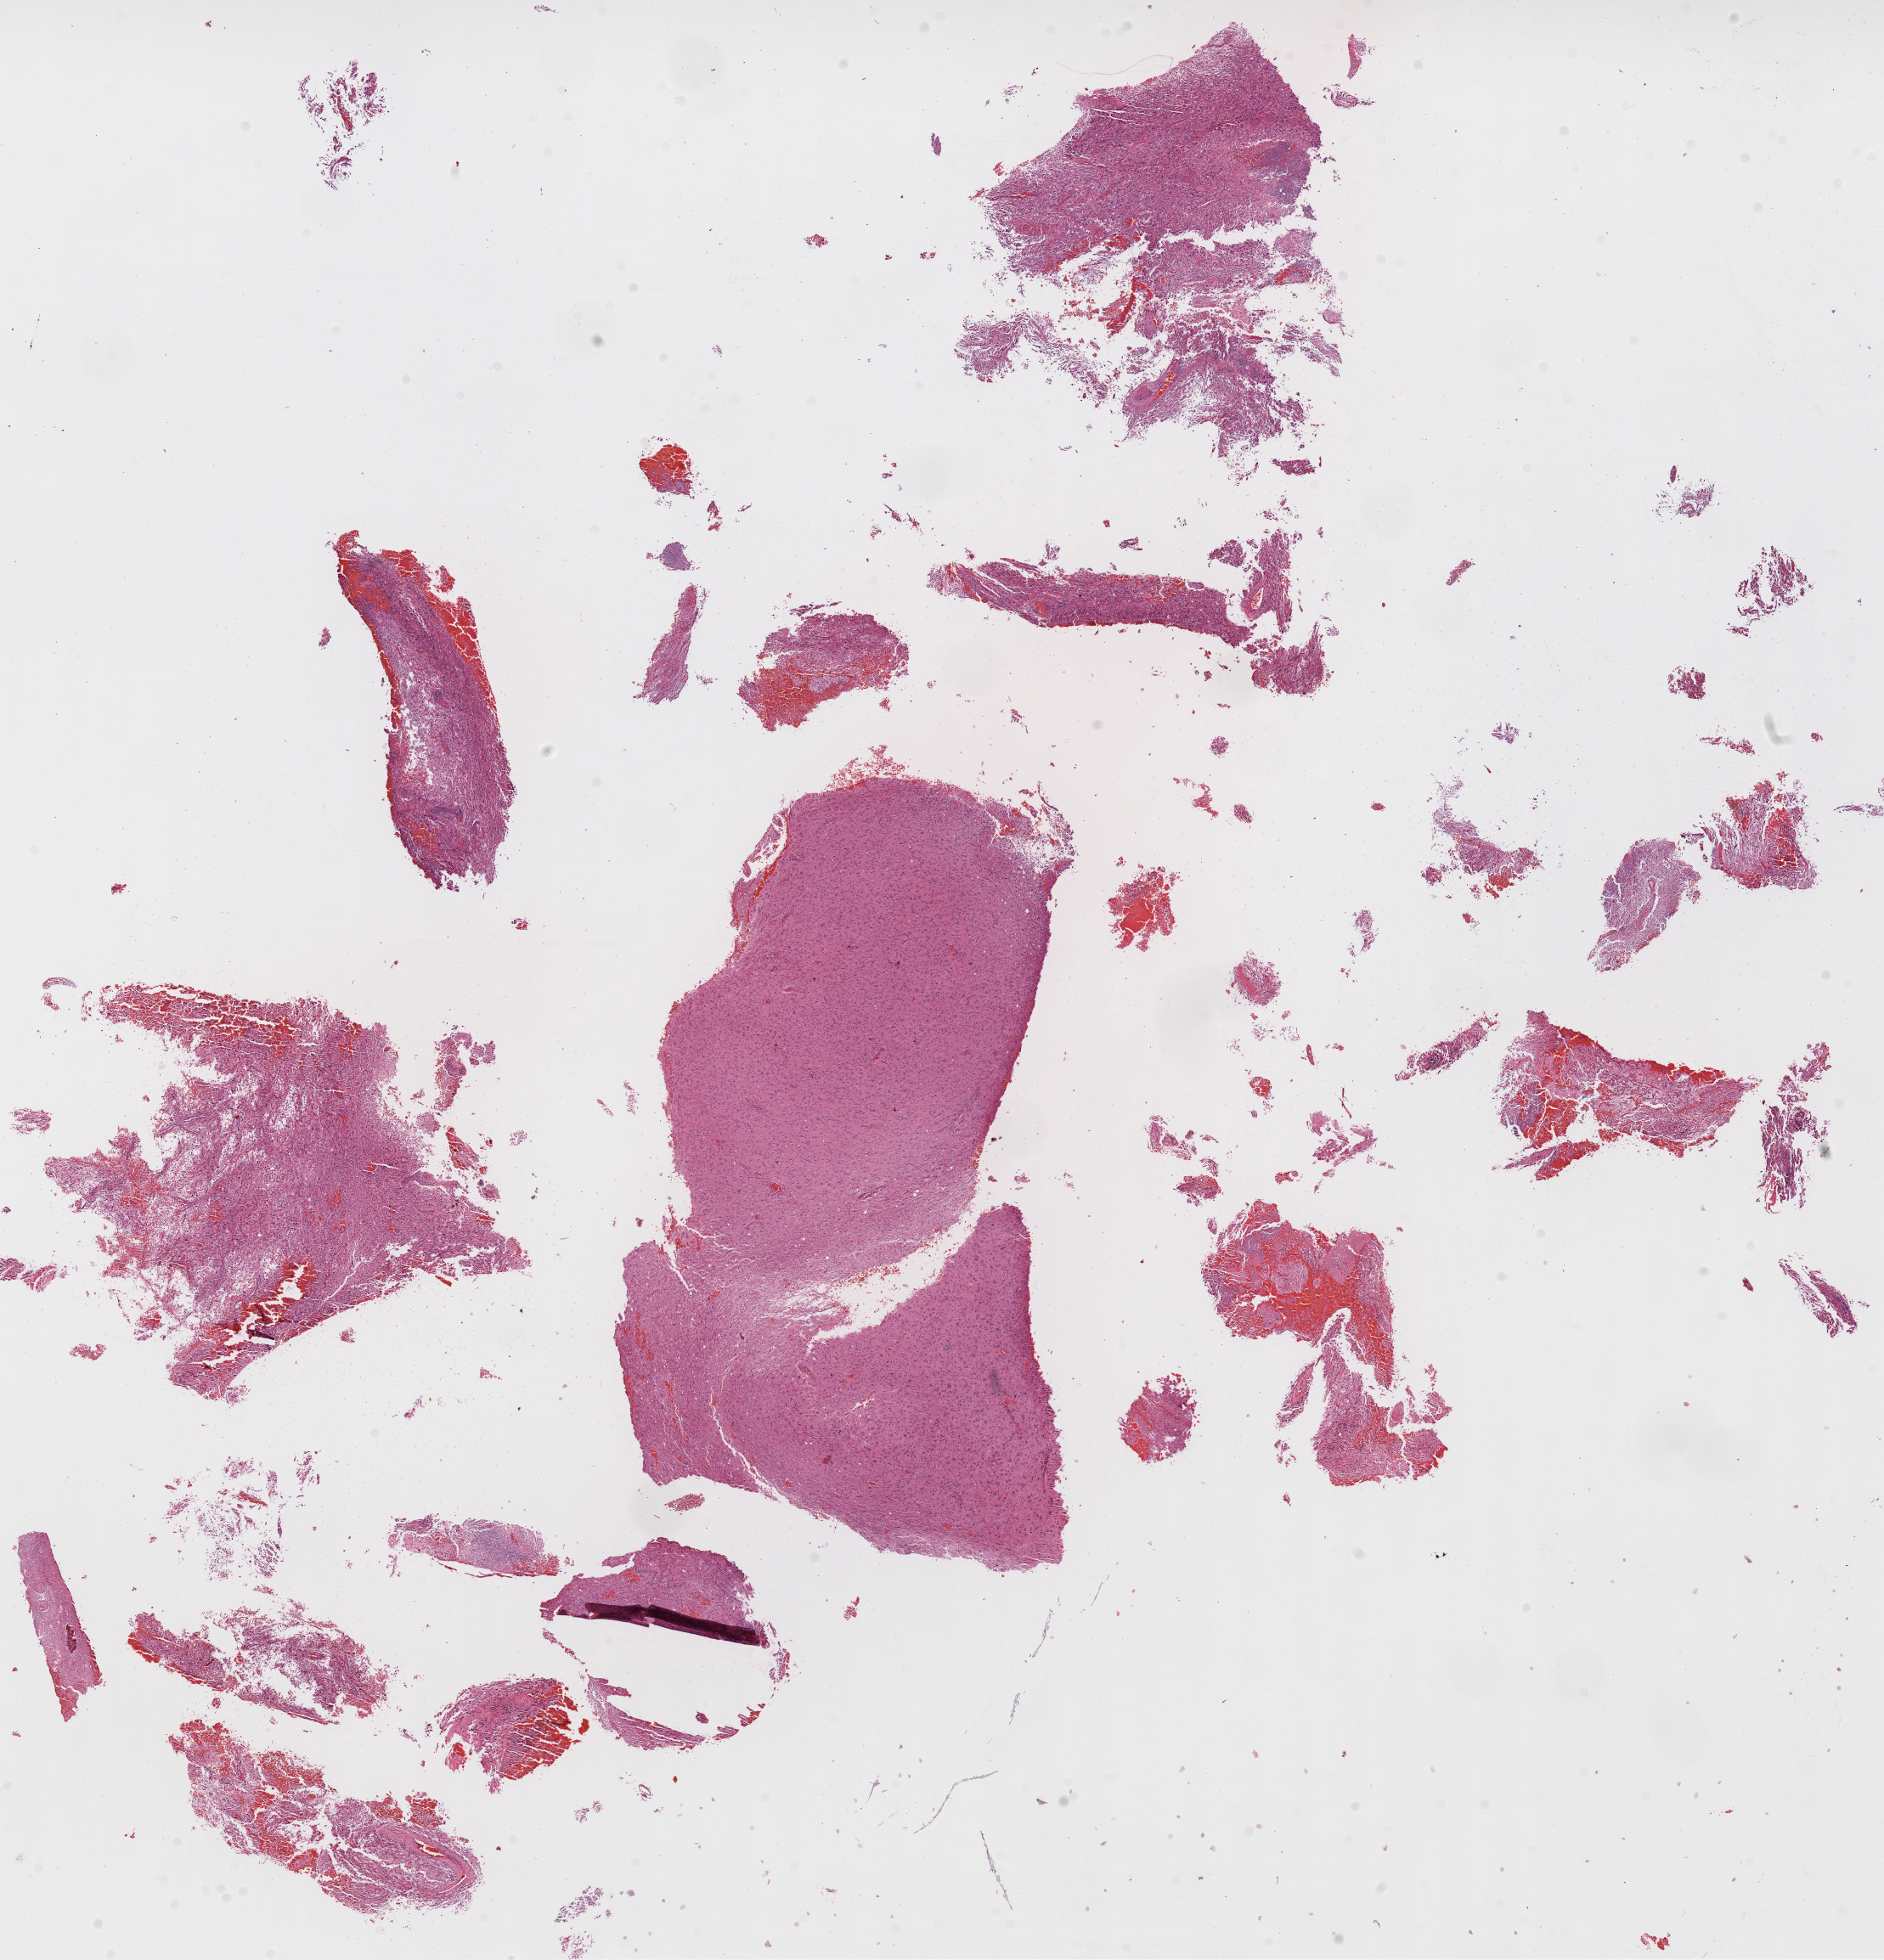
Whole-slide histology image, Hematoxylin and eosin (H&E) stained — shown as a low-resolution overview of the whole scanned area (about 17.9 x 18.6 mm), FFPE section, brain, primary tumour sample. Male, age 62 years at initial diagnosis.
Diagnosis: Glioblastoma.